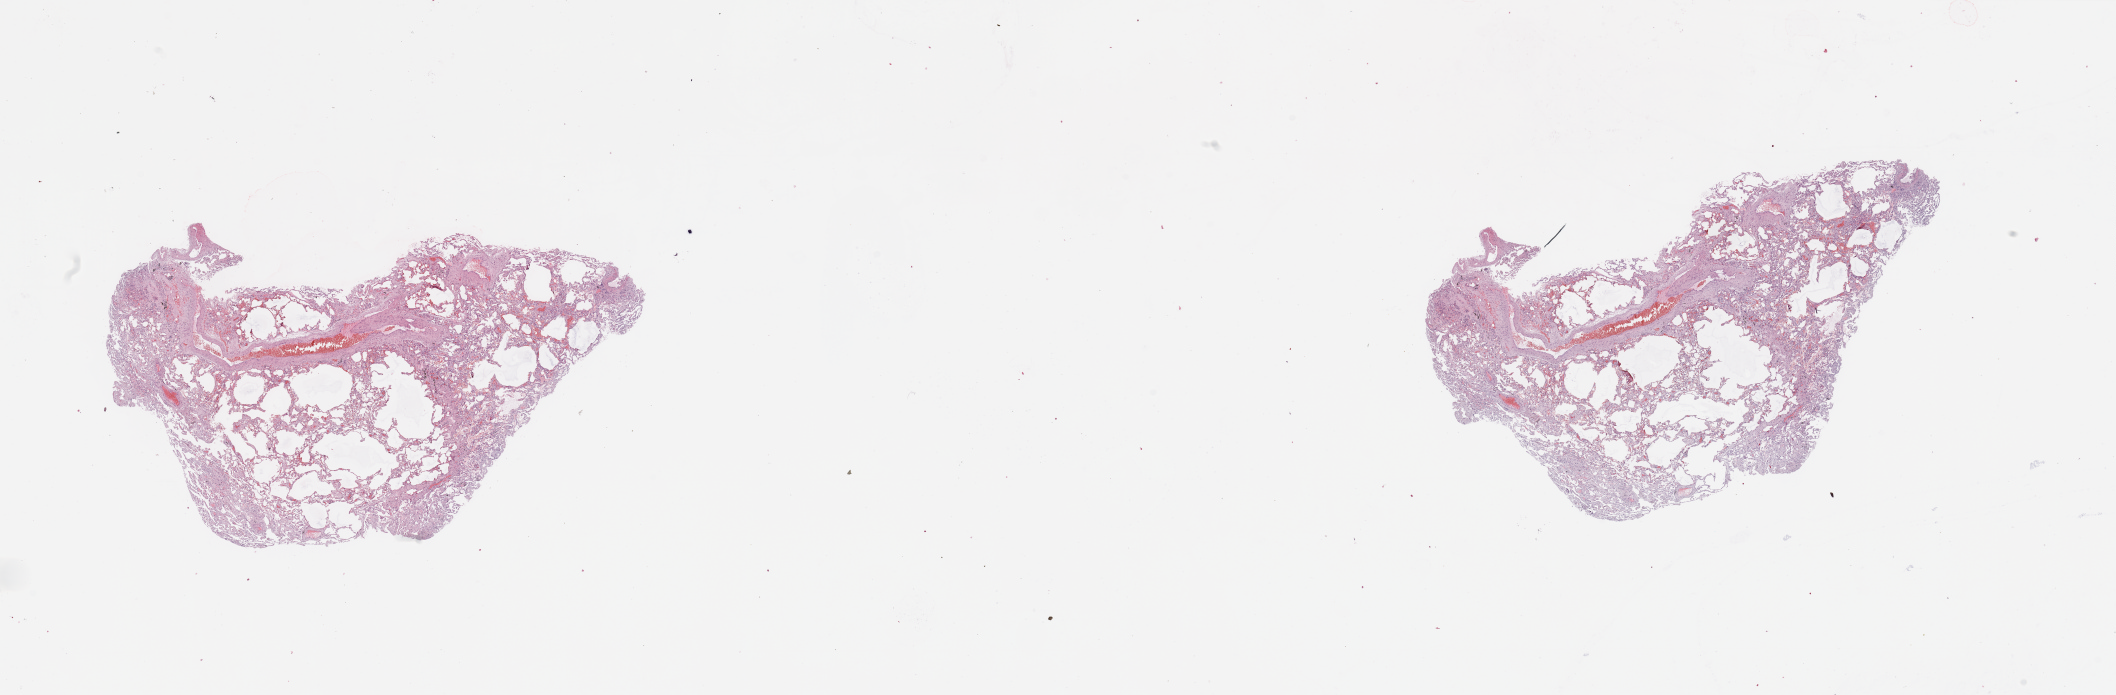
Digitized H&E tissue section (whole slide), whole scanned area (about 33.5 x 11.0 mm, slide scanned at 20x) shown as a low-resolution overview, normal (non-tumour) tissue sample, lung. 72-year-old male patient.
This section: normal (non-tumour) tissue from the same patient. Patient diagnosis: Squamous cell carcinoma, NOS.